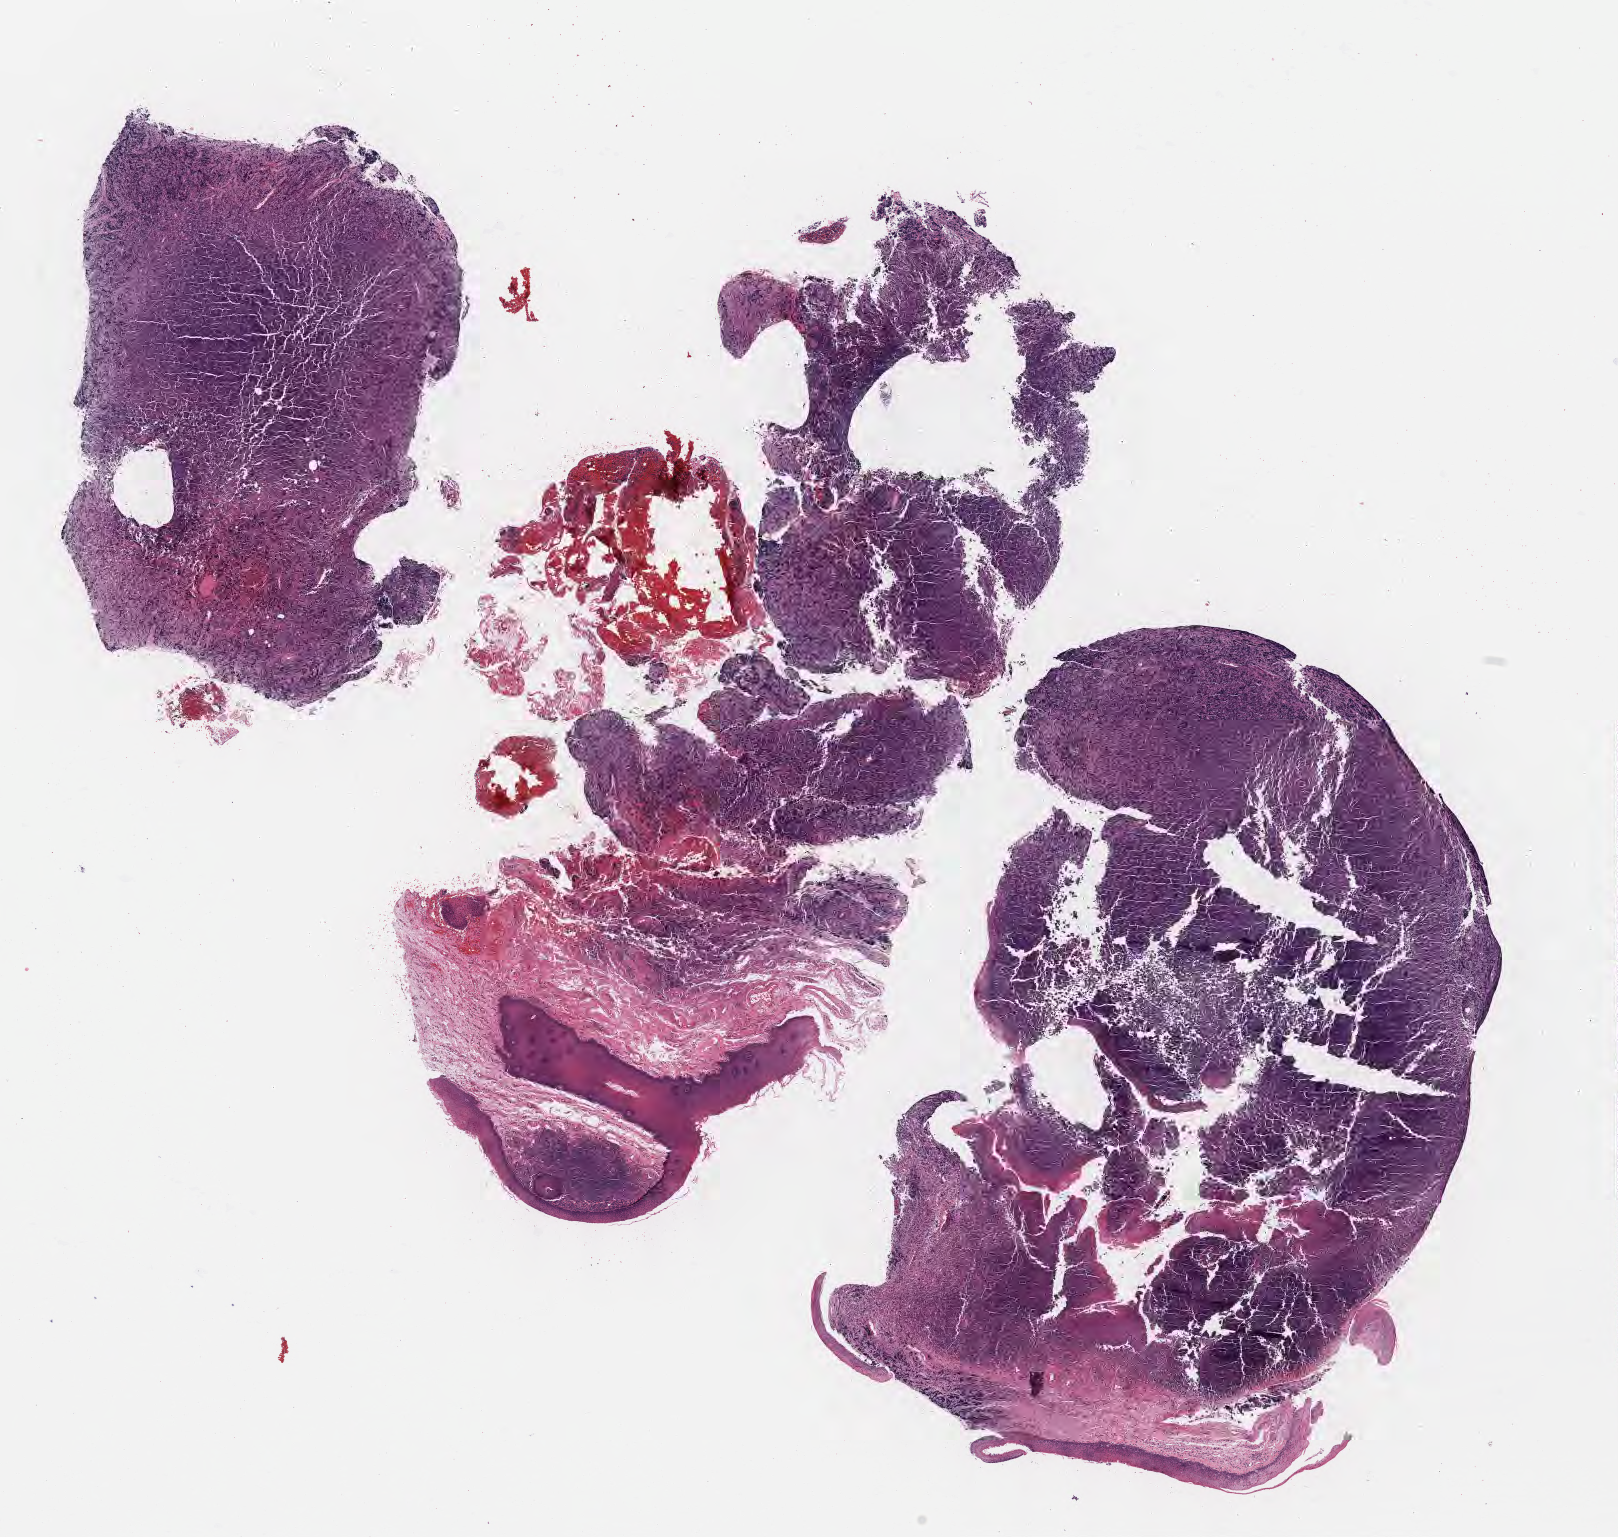
Digitized H&E-stained section, whole scanned area (about 13.1 x 12.4 mm) shown as a low-resolution overview. Tumor tissue. Patient: male, 63 years old.
Histologic diagnosis: Burkitt lymphoma, NOS.